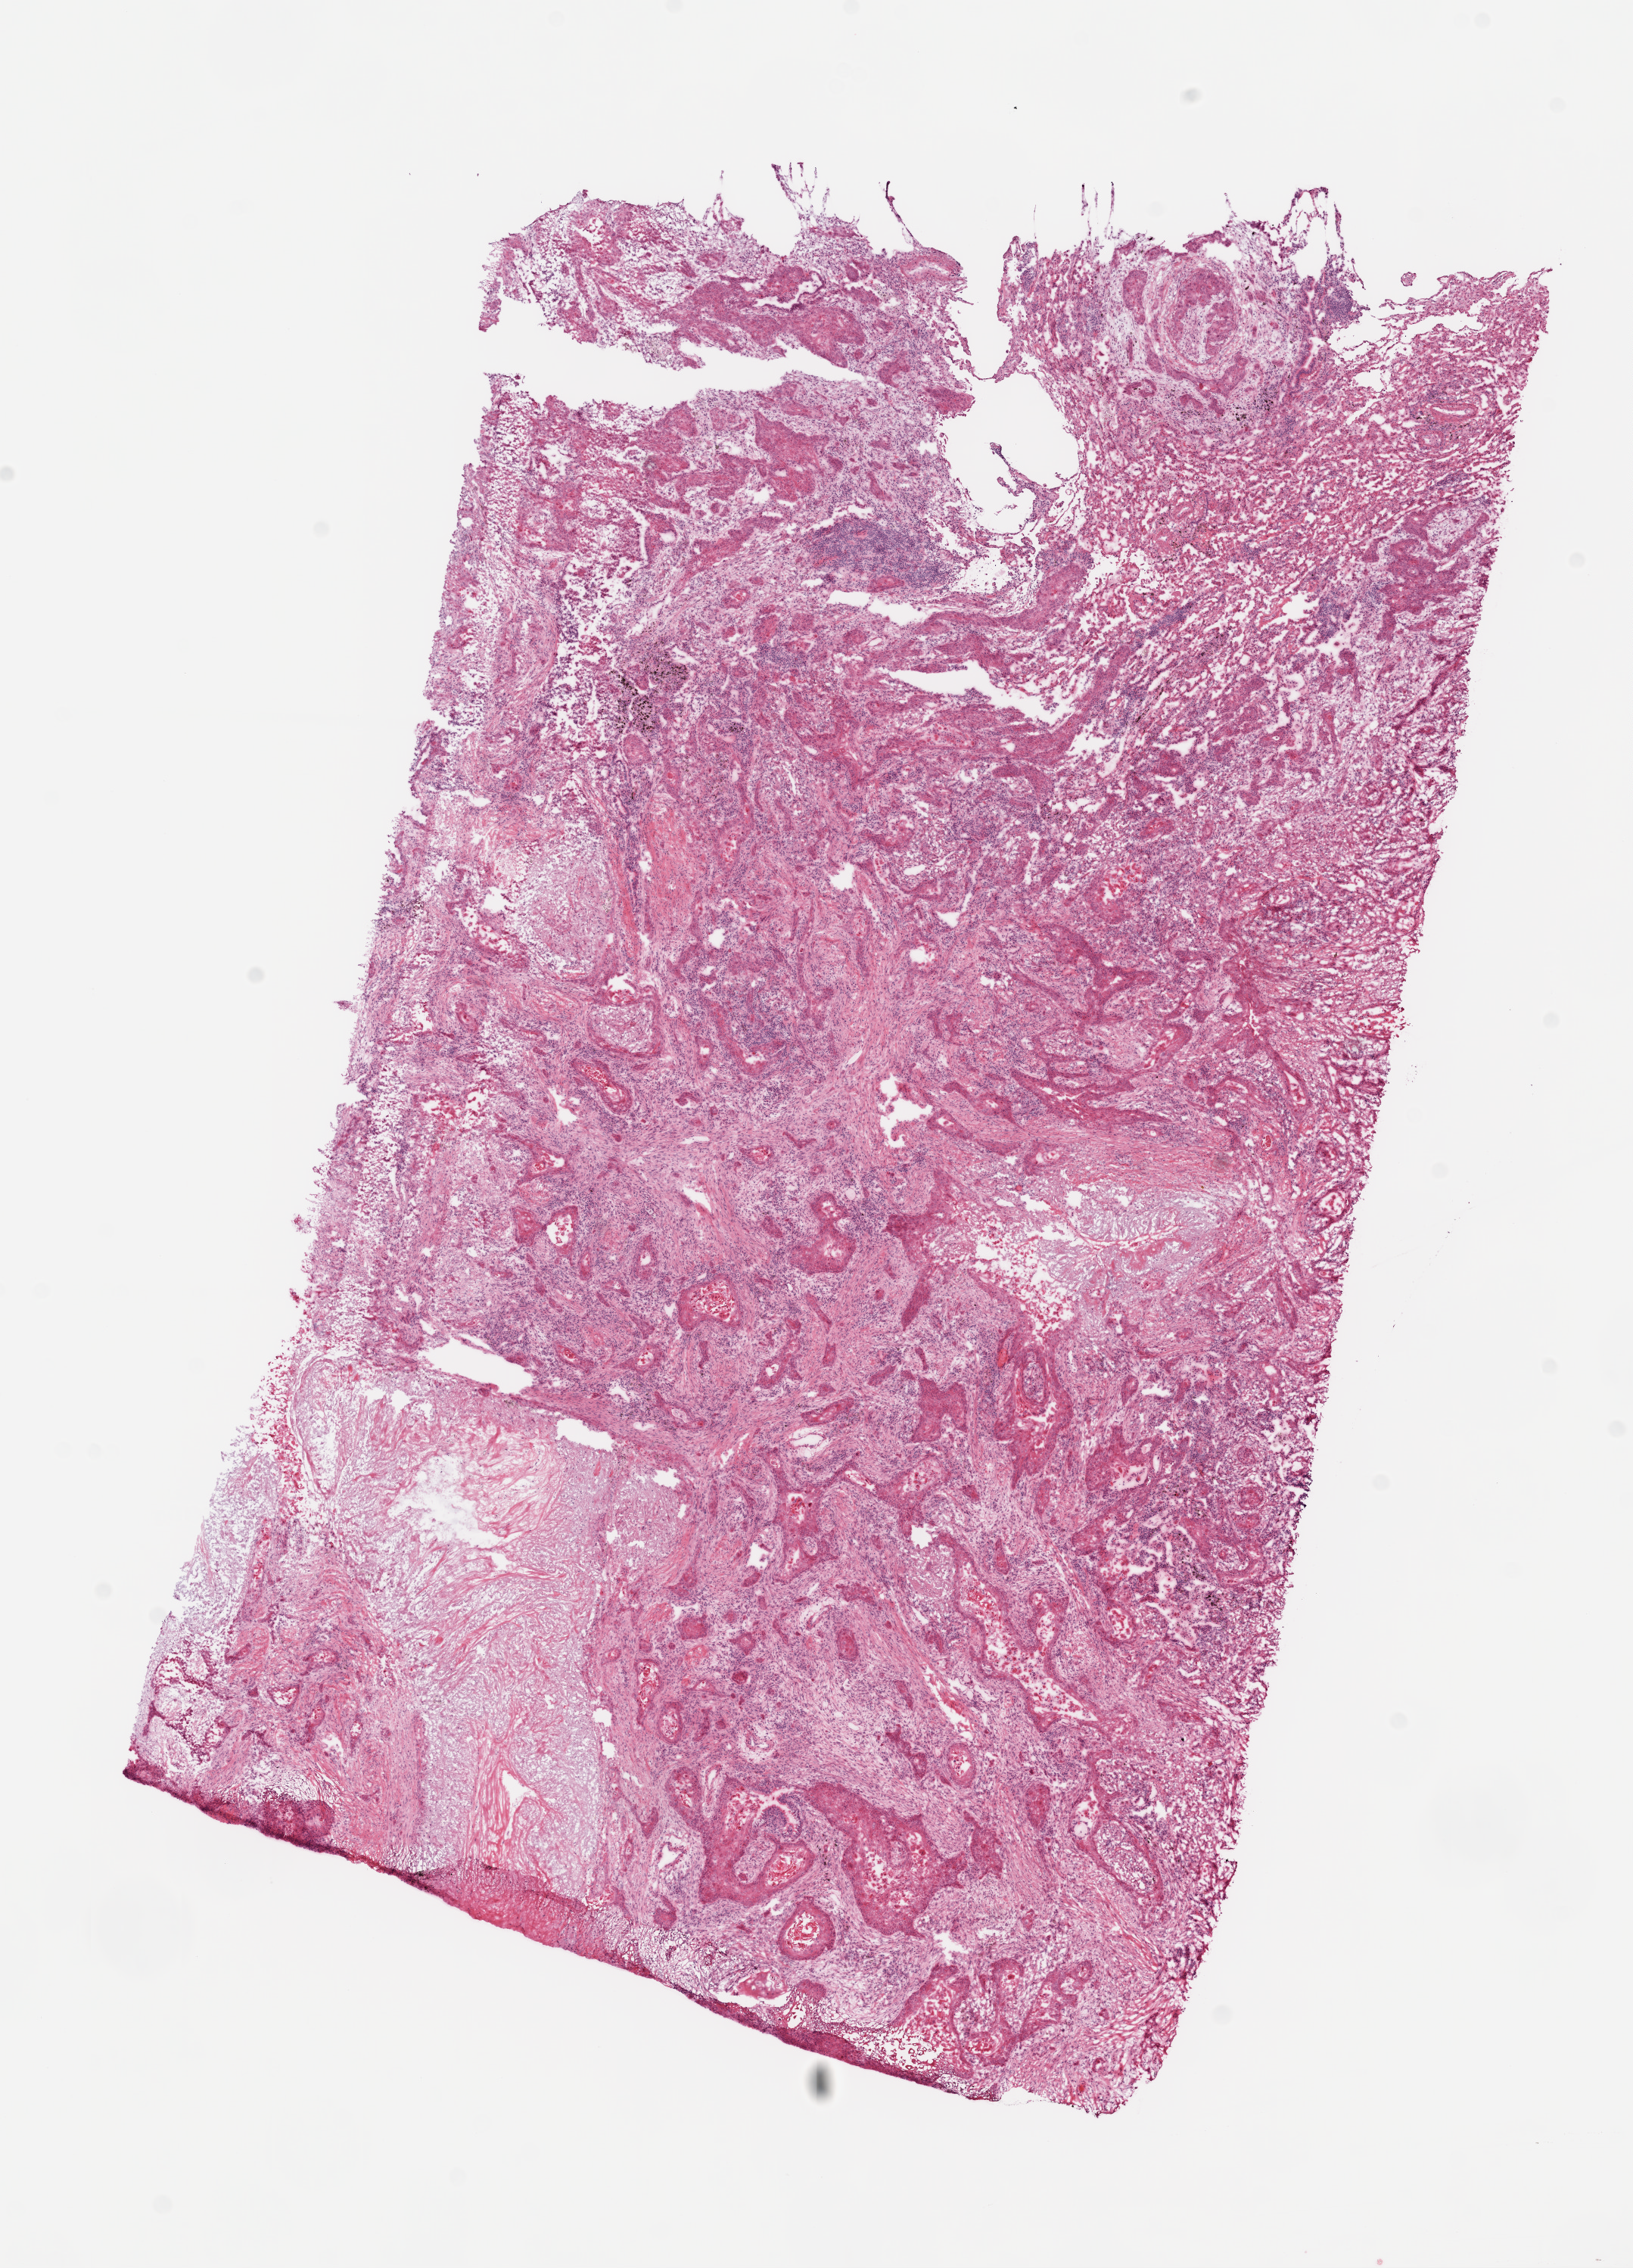
H&E whole-slide image — shown as a low-resolution overview of the whole scanned area (about 8.7 x 12.1 mm); frozen section from the top of the tissue portion; sample: primary tumour, lung. Male, age 76 years at initial diagnosis. Slide review estimates, as recorded: tumour nuclei 70%, necrosis 15%.
Diagnosis: Squamous cell carcinoma, NOS. AJCC pathologic stage: IB (7th edition).